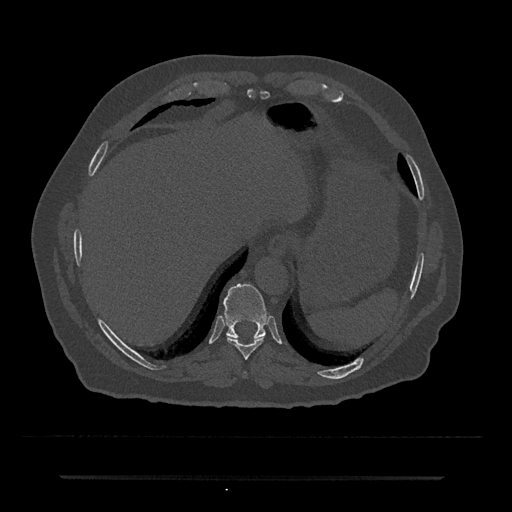
CT including the spine, one axial slice; slice 257 of 797 in the series (ordered by position); reconstruction kernel Br40s/3; 120 kVp; bone window (W 1800 / L 400 HU); 0.5 mm slice thickness; 512 × 512 image matrix, field of view 437 × 437 mm. Patient: male, 69 years. From the clinical record (not read from this slice): primary cancer: prostate.
Outlined on this slice (semi-automatic segmentation, software-assisted and operator-edited):
- T10 vertebra: bounding box [x1, y1, x2, y2] px = [223, 284, 267, 339]
- T9 vertebra: [227, 336, 264, 360]